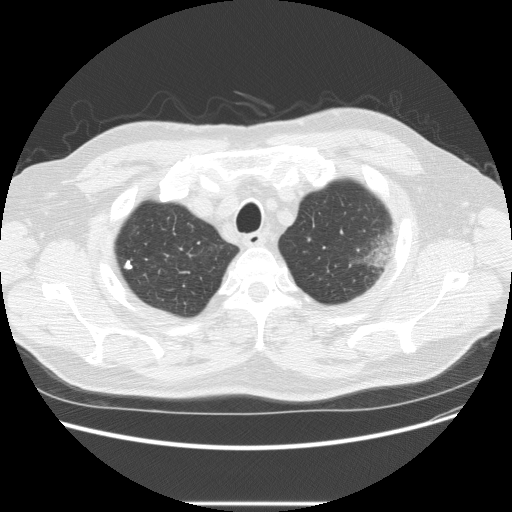
Axial slice from a low-dose chest CT screening exam, baseline annual screen, lung window (W 1500 / L -600 HU), 120 kVp. Male, age 73 years at enrolment. Former smoker at enrolment.
Expert reader's lesion annotation, bounding box <331,216,406,283> (left, top, right, bottom; pixels). The screening reader recorded 2 non-calcified nodules or masses ≥4 mm on this exam (left upper lobe, right upper lobe); which of them this box marks is not recorded. Later outcome: lung cancer diagnosed 11 days after this screen — bronchiolo-alveolar adenocarcinoma, NOS, other location, well differentiated (G1), stage IV (AJCC 6th edition).